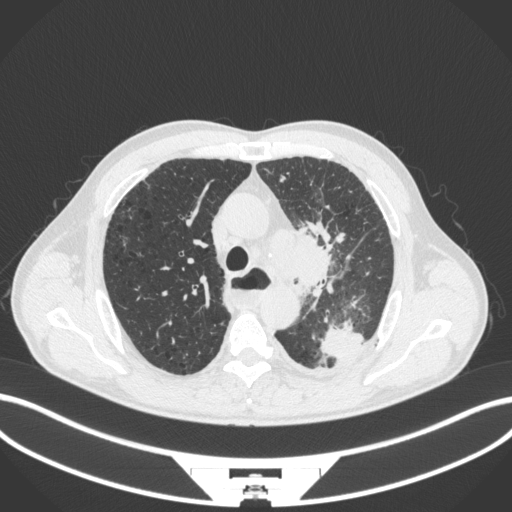
Chest CT, one axial slice. Slice 276 of 411 in the series (ordered by position). 120 kVp. Lung window (W 1500 / L -600 HU). 512 × 512 image matrix. Male patient, age 57 years. Case-level facts recorded for this patient, not image findings: clinical TNM (as recorded): T2a N1 M0.
Outlined on this slice (rectangle marked by the reading radiologist):
- lung tumour (recorded histology: squamous cell carcinoma): box from (x=265, y=226) to (x=338, y=293) px